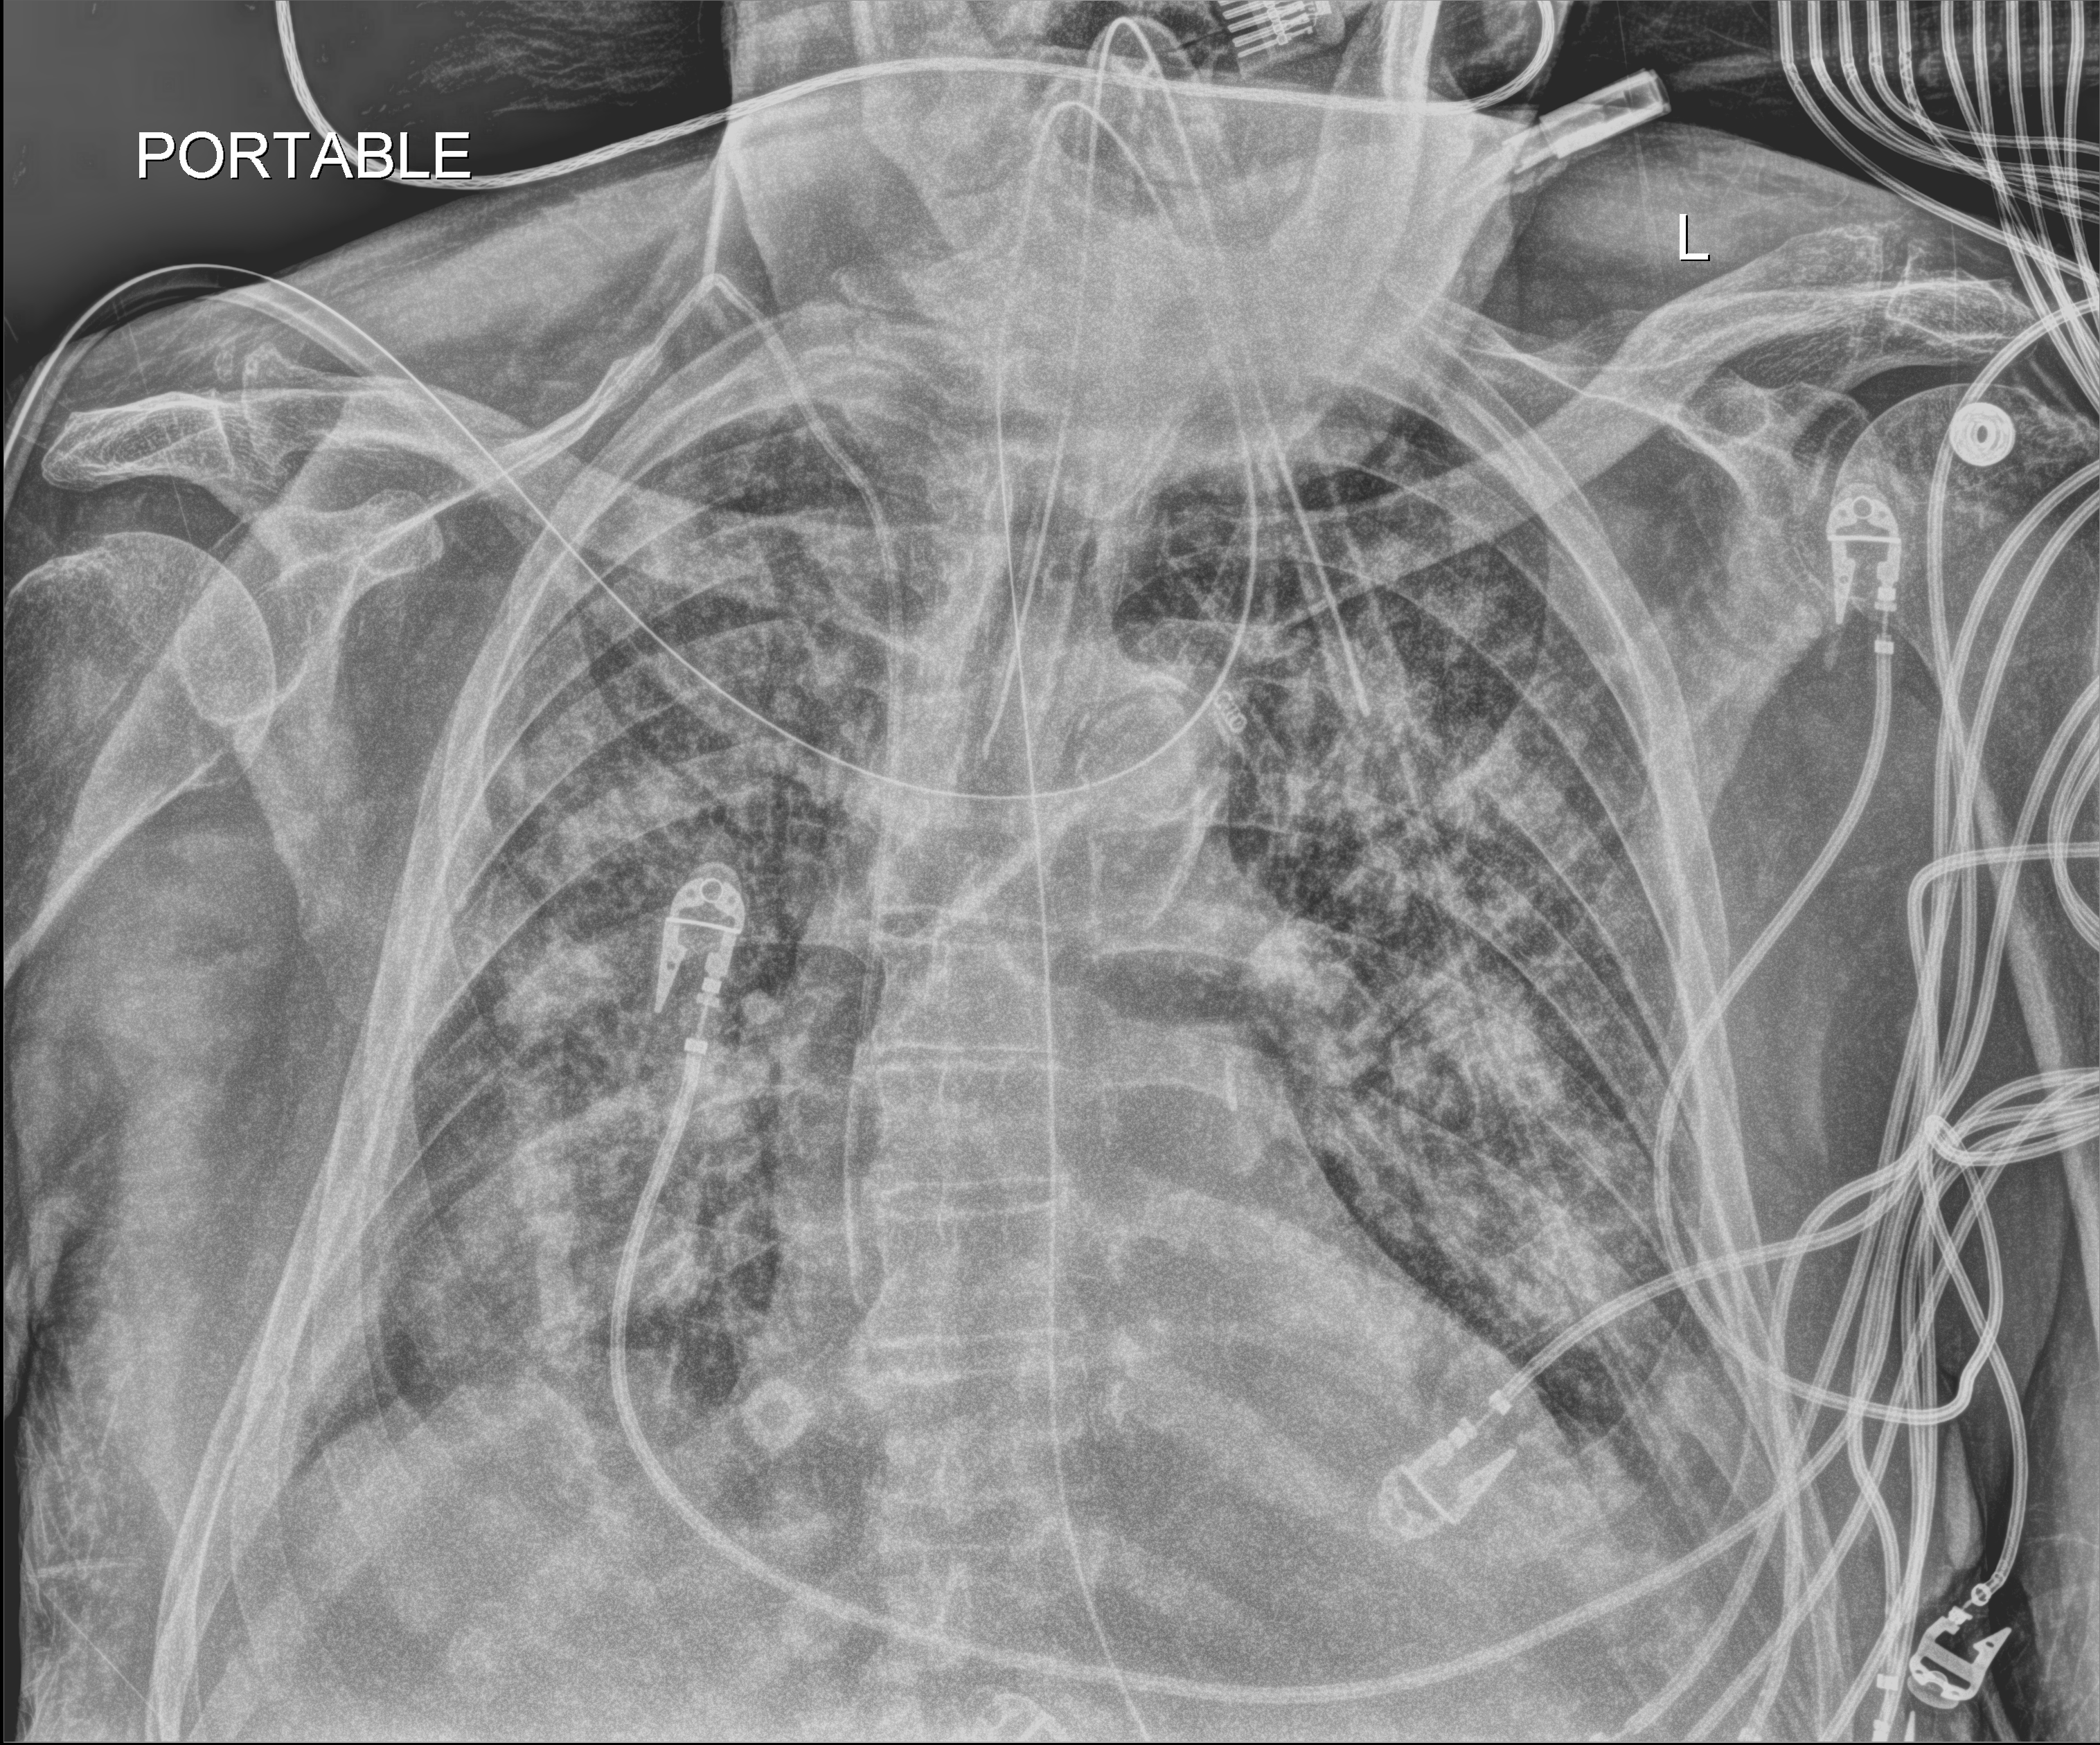
Bedside chest radiograph (digital radiography), anteroposterior (AP) projection. Patient hospitalised with COVID-19; male, aged 75–90 years.
Admission-level facts for this patient (not findings on this image; timing relative to this image not recorded): smoking status (admission record): never; length of hospital stay: 28 days.